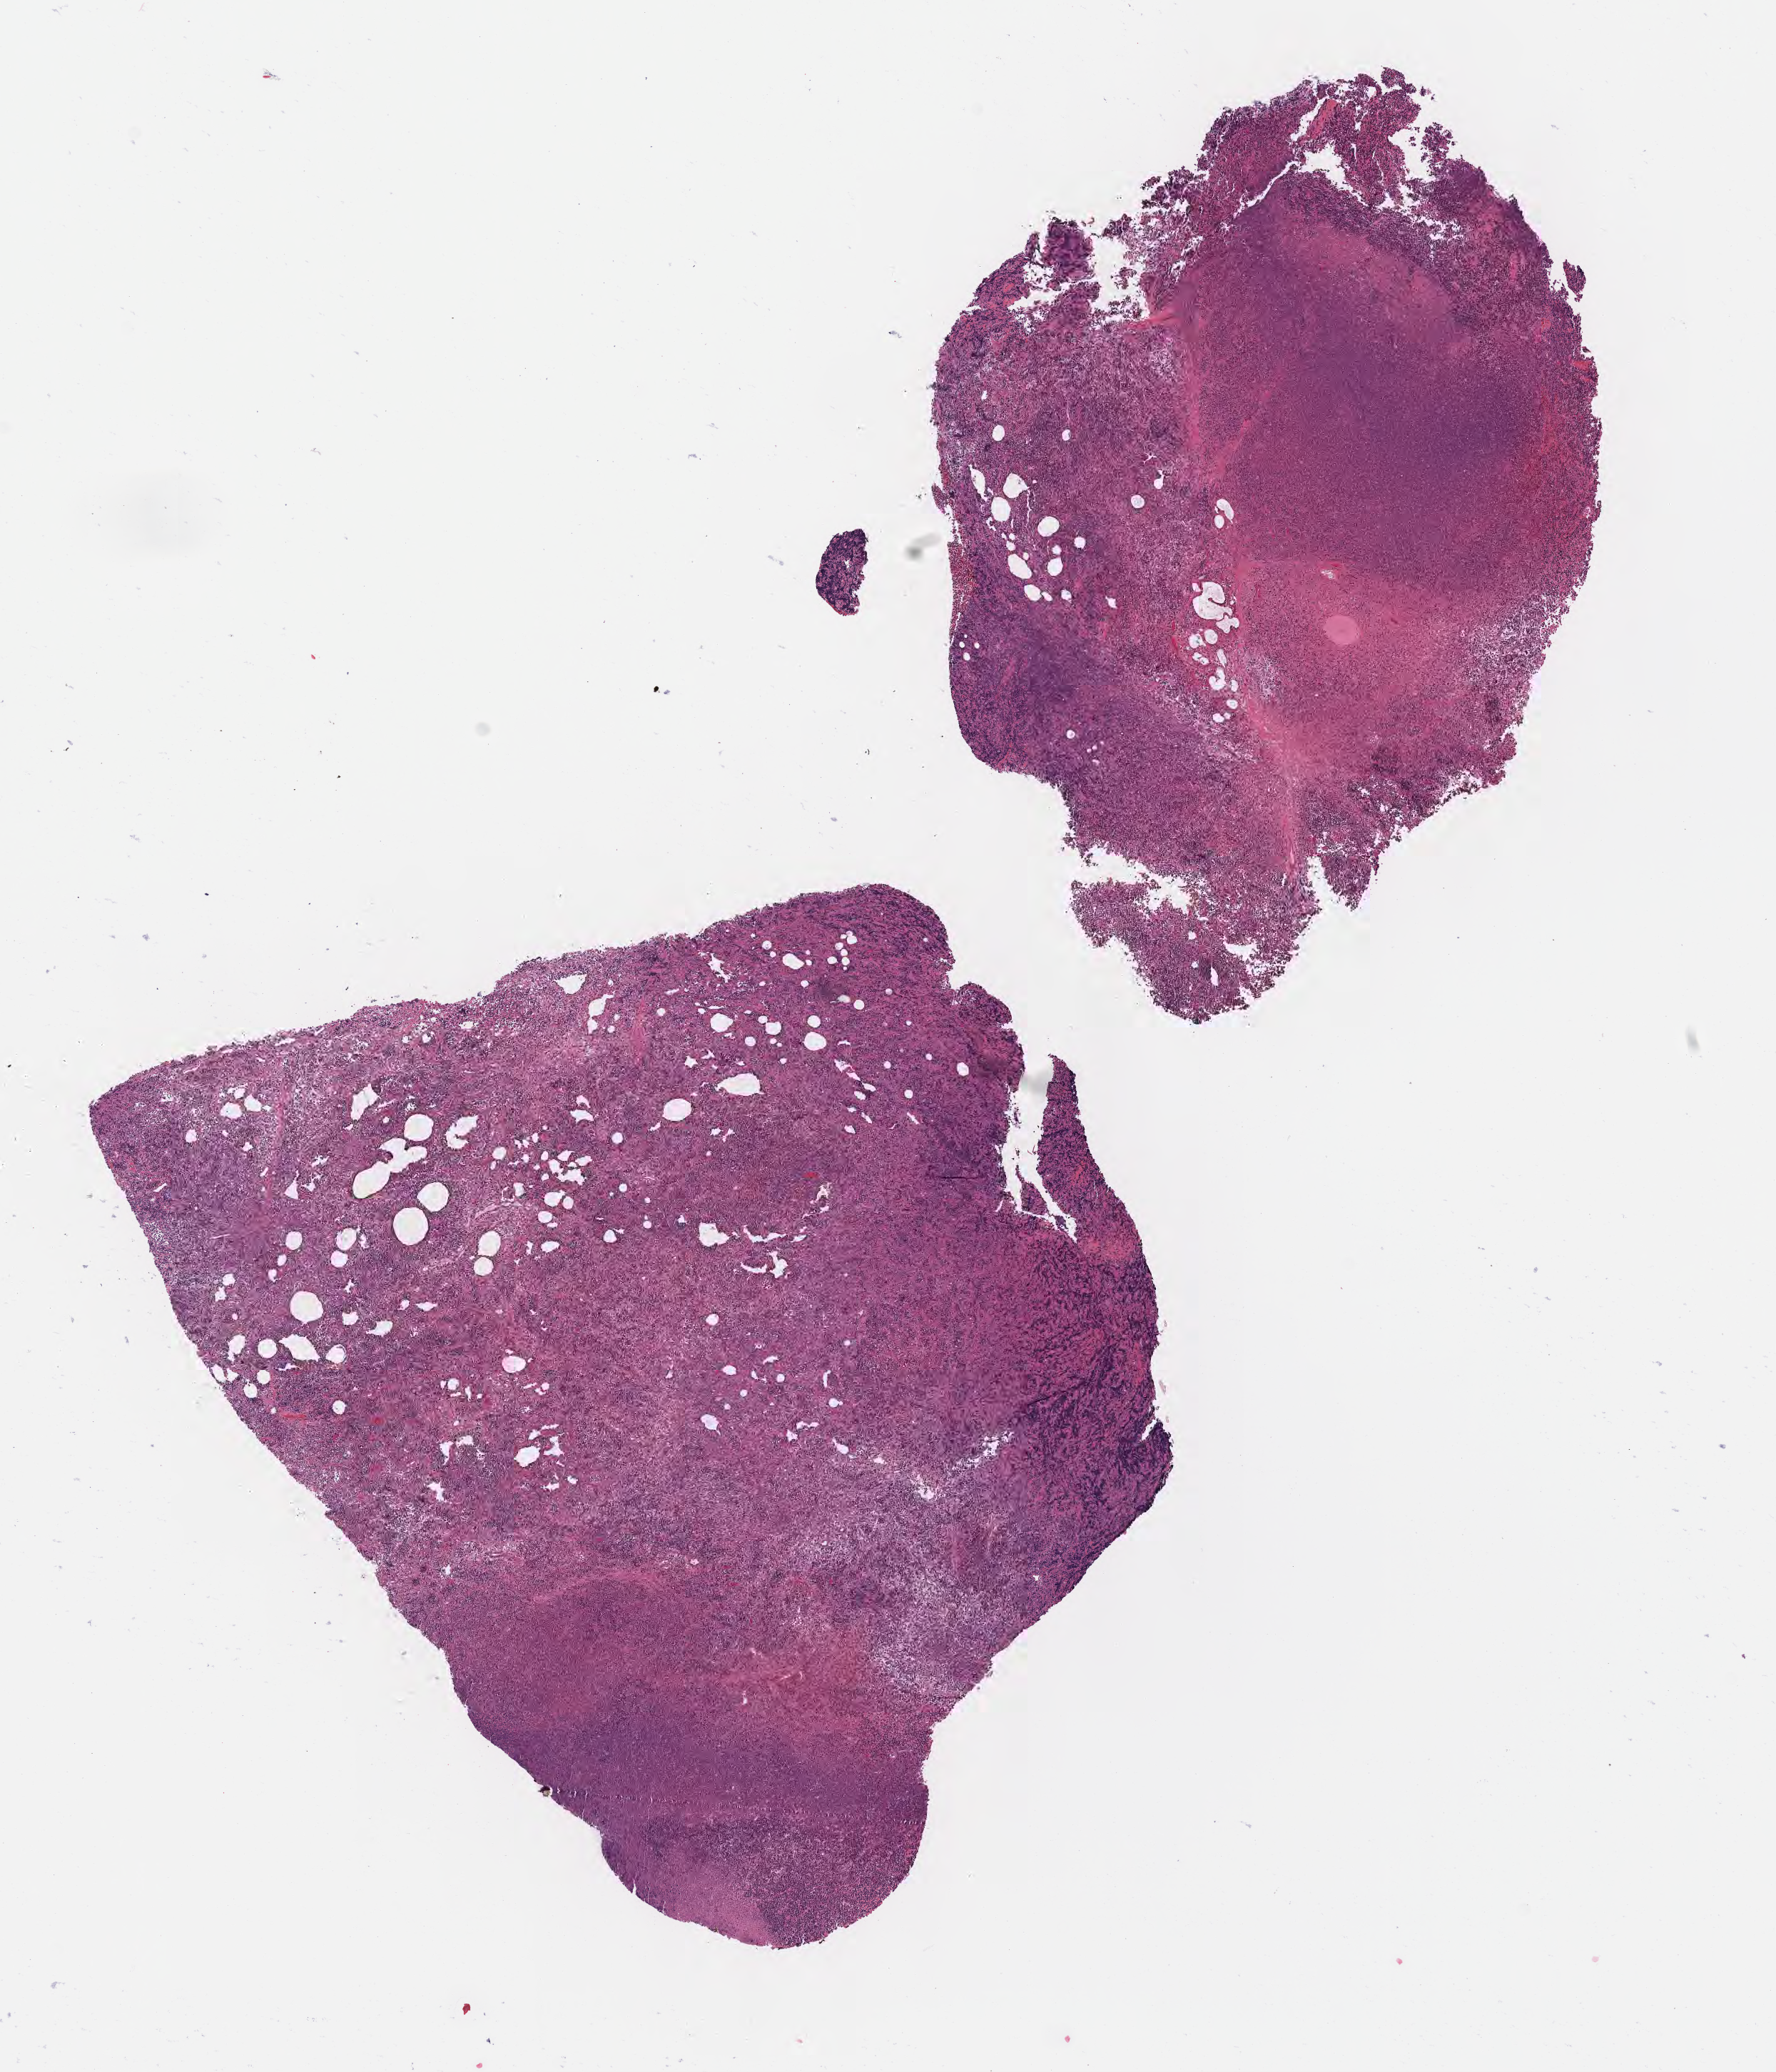
Digitized haematoxylin and eosin-stained section — whole scanned area (about 10.1 x 11.7 mm) shown as a low-resolution overview, specimen: tumor tissue, anatomic site: mandible. Male, age 7 years at initial diagnosis.
* diagnosis: Burkitt lymphoma, NOS